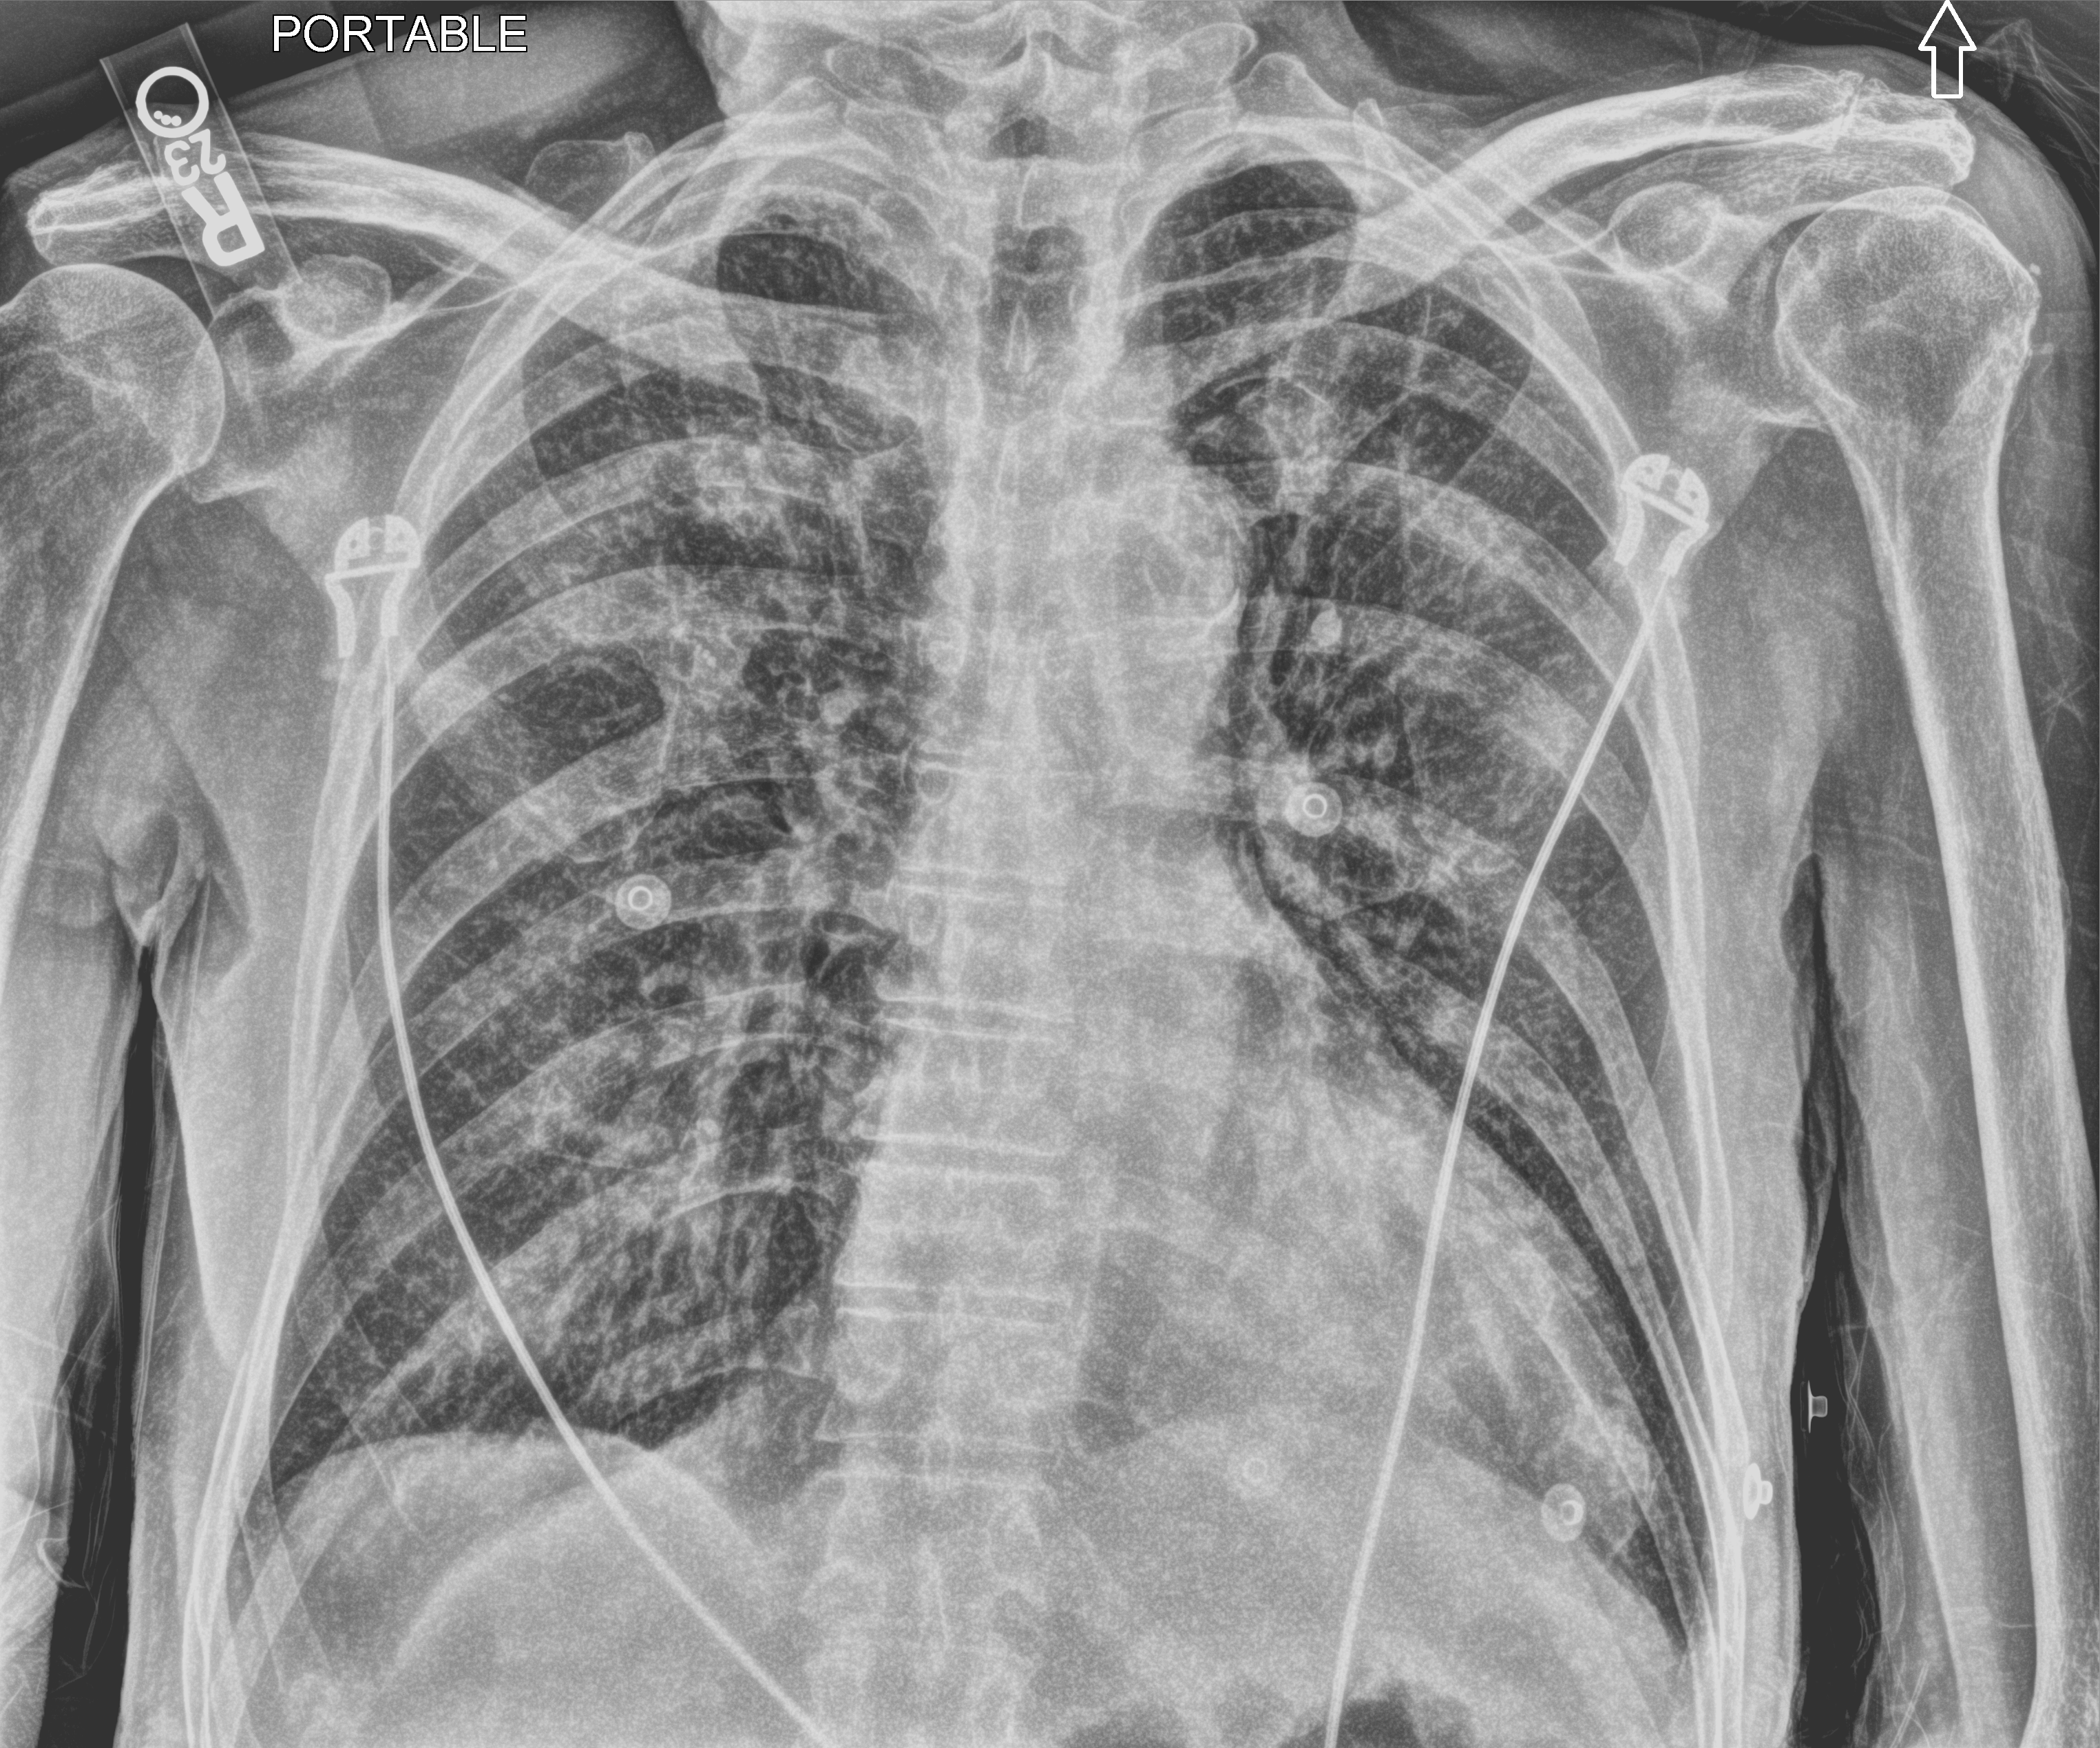
Chest X-ray (portable); anteroposterior (AP) projection. Patient hospitalised with COVID-19; male, aged 75–90 years.
Admission-level facts for this patient (not findings on this image; timing relative to this image not recorded):
- mechanically ventilated during this hospital stay: no